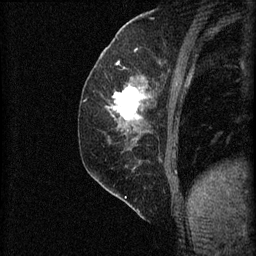
Breast MRI (dynamic contrast-enhanced), one sagittal slice. Slice 27 of 60 in the series (ordered by position). 3 images stored at this slice position (order not interpretable as contrast timing). 1.5 T. TE 4.2 ms, TR 8.2 ms. 2 mm slice thickness. 256 × 256 image matrix, field of view 180 × 180 mm. Female patient, age 59 years.
Annotated regions visible in this slice (semi-automatically segmented with operator editing):
- analysis volume of interest (the breast-tissue region the enhancement analysis was run in; not a lesion): bounding box <108,74,155,131> (left, top, right, bottom; pixels)
- tumour enhancement mask (voxels above the 70 % enhancement threshold inside the analysis volume of interest): <108,86,148,121>